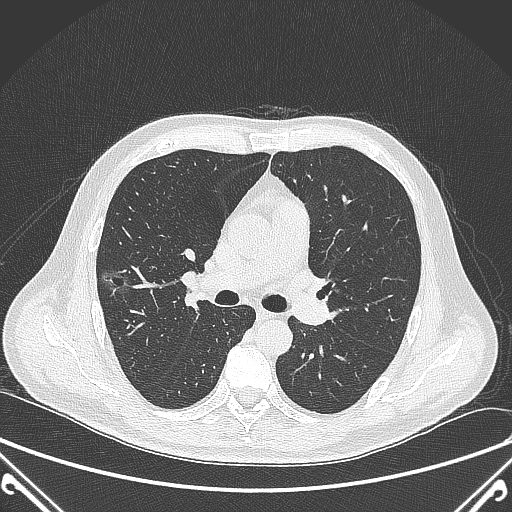
Chest CT, one axial slice. Position 223 of 360 along the scan axis. Lung window (W 1500 / L -600 HU). 1 mm slice thickness. 512 × 512 image matrix, field of view 380 × 380 mm. Male patient, age 64 years. From the clinical record (not read from this slice): clinical TNM (as recorded): T1c N0 M0.
Structures marked on this image (bounding box drawn by a radiologist):
- lung tumour (recorded histology: adenocarcinoma): bounding box (x1, y1, x2, y2) in pixels: (99, 262, 144, 305)